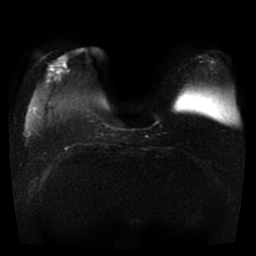
Breast MRI, one axial slice. Slice 9 of 41 in the series (ordered by position). Diffusion-weighted series; image 2 of 4 stored at this slice position (different b-values; order by instance number). 1.5 T. 5 mm slice thickness. 256 × 256 image matrix, field of view 330 × 330 mm. Female patient.
Structures marked on this image (manually delineated by an expert):
- tumour on diffusion-weighted imaging: box from (x=53, y=67) to (x=63, y=73) px